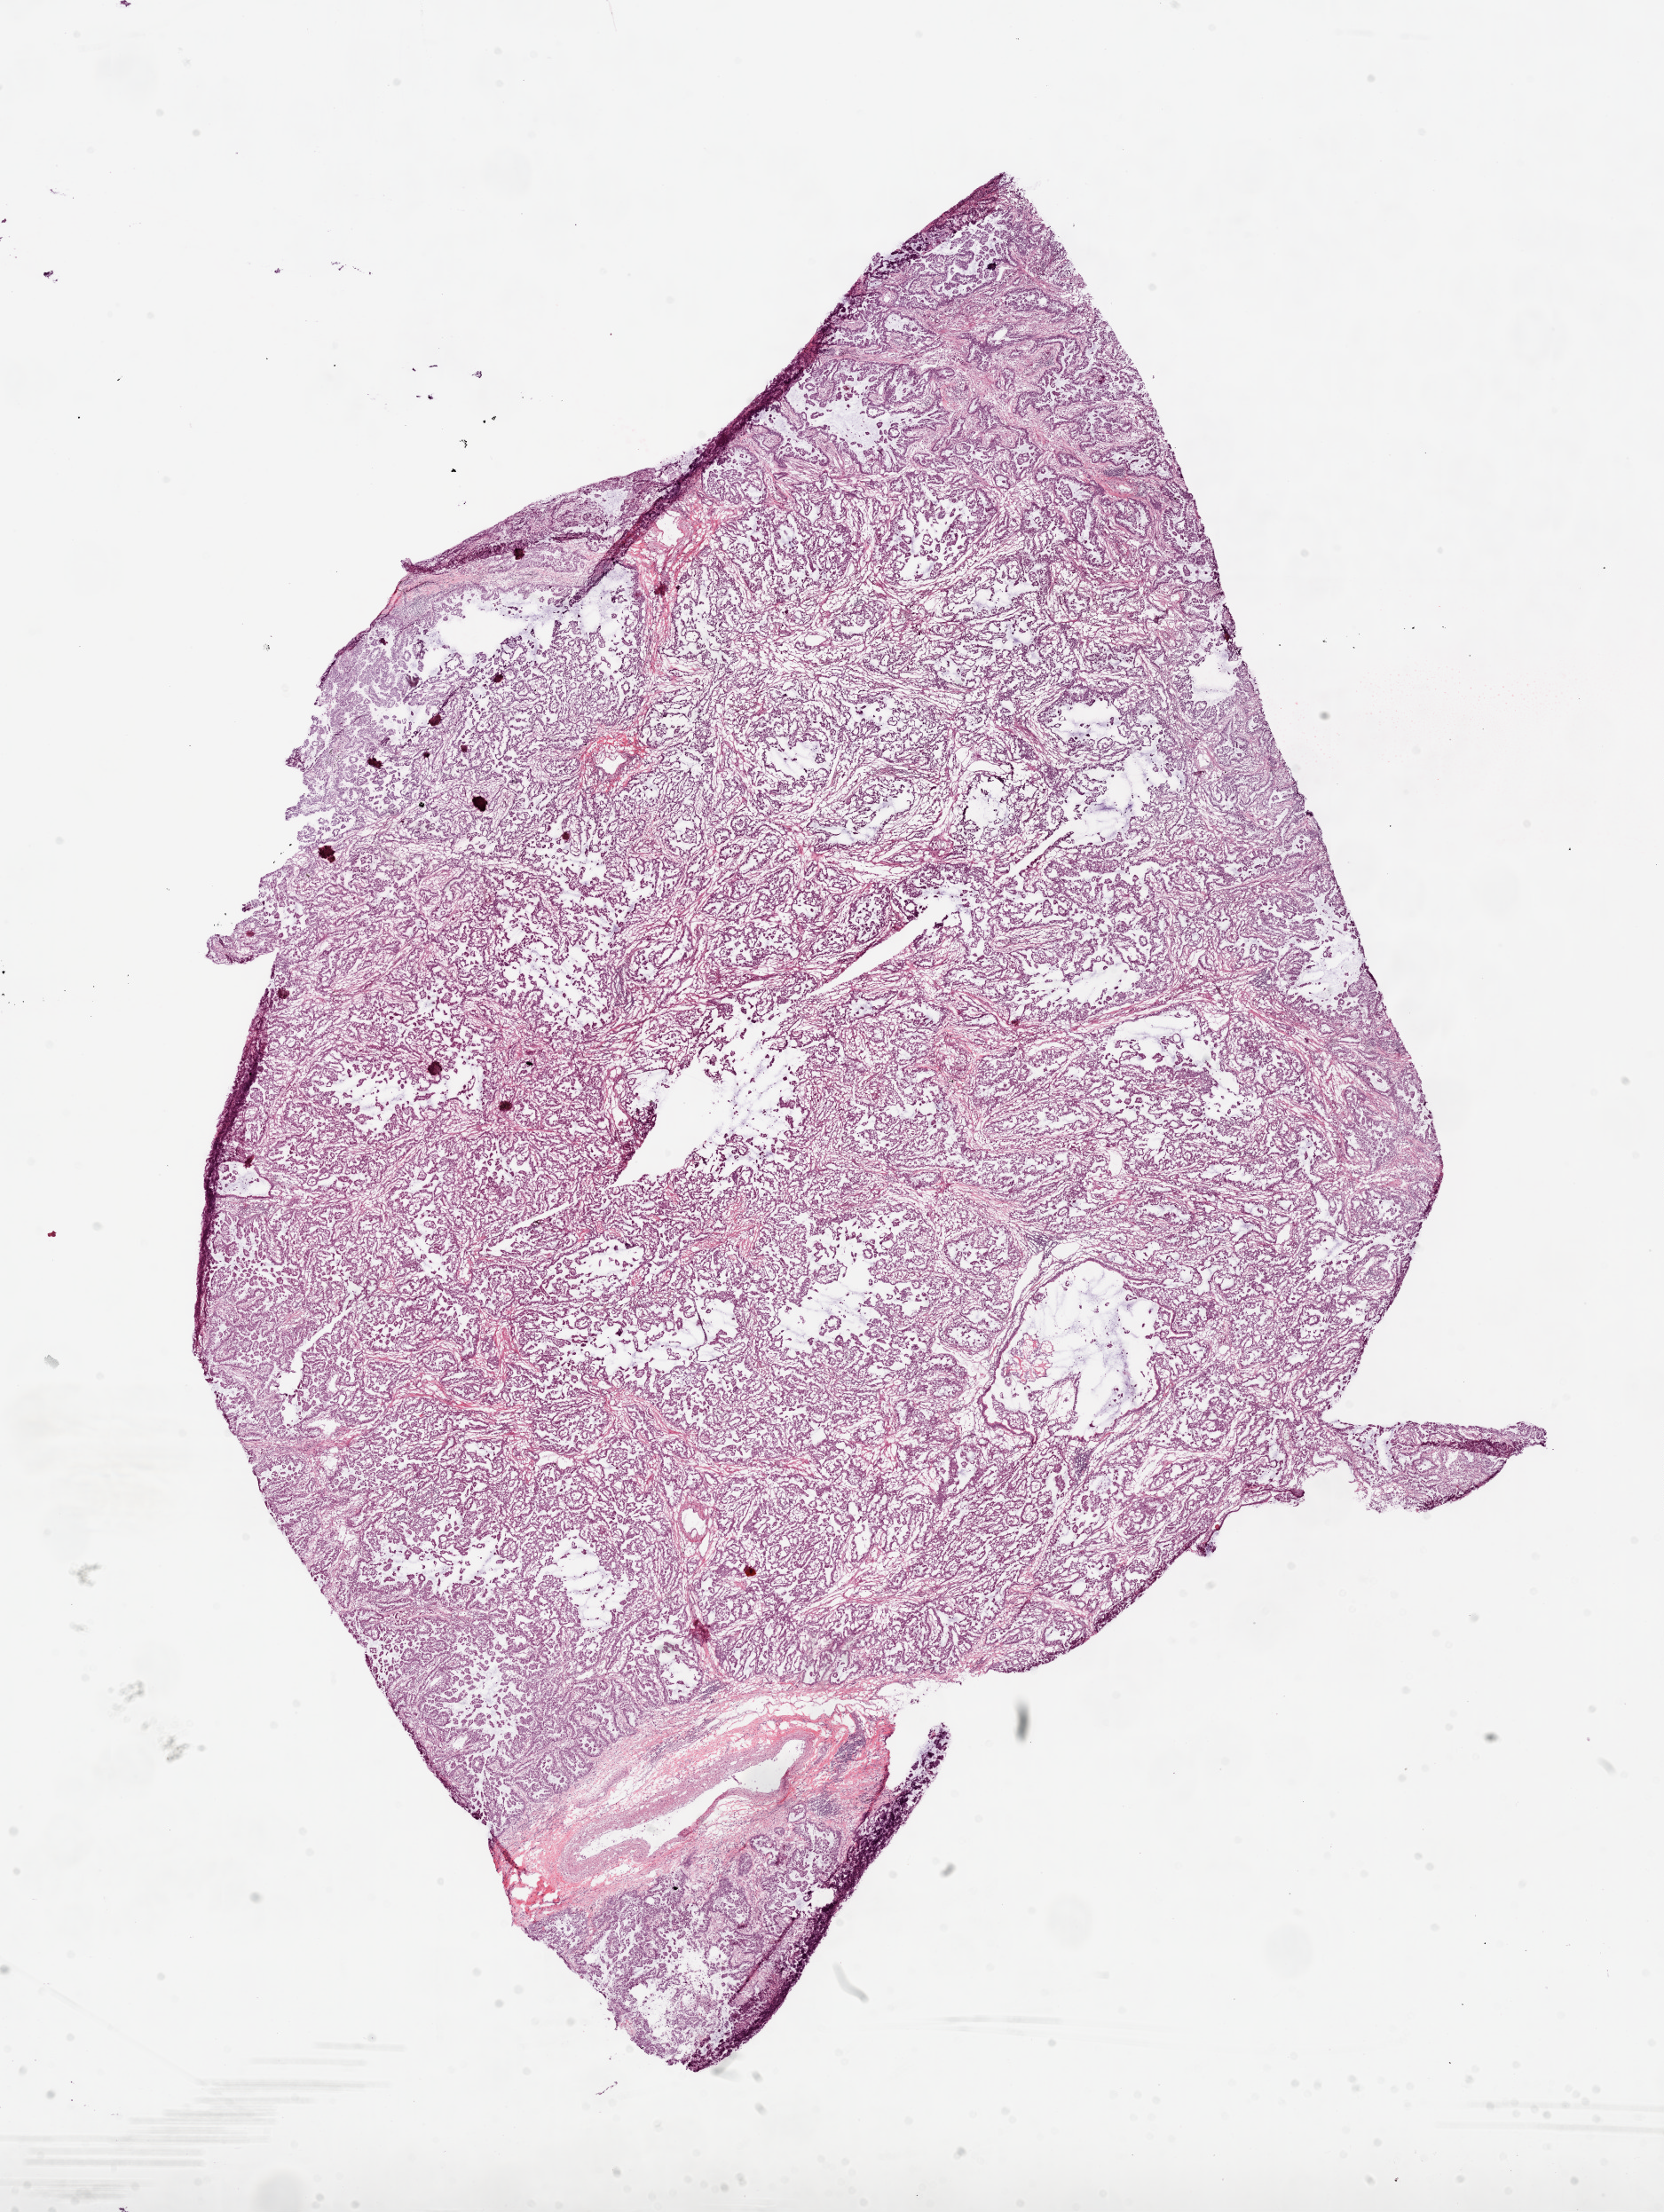
Hematoxylin and eosin (H&E) stained whole-slide image, shown as a low-resolution overview of the whole scanned area (about 15.0 x 20.0 mm, from a 20x scan), frozen section from the top of the tissue portion, lung, primary tumour sample. Male patient; age at initial diagnosis 59 years. Slide review estimates, as recorded: tumour cells 50%, tumour nuclei 80%, normal cells 0%, stromal cells 50%, necrosis 0%.
* AJCC pathologic stage: IIIA (7th edition)
* pathologic diagnosis: Adenocarcinoma, NOS (lower lobe, lung)
* TNM: T3 N1 M0